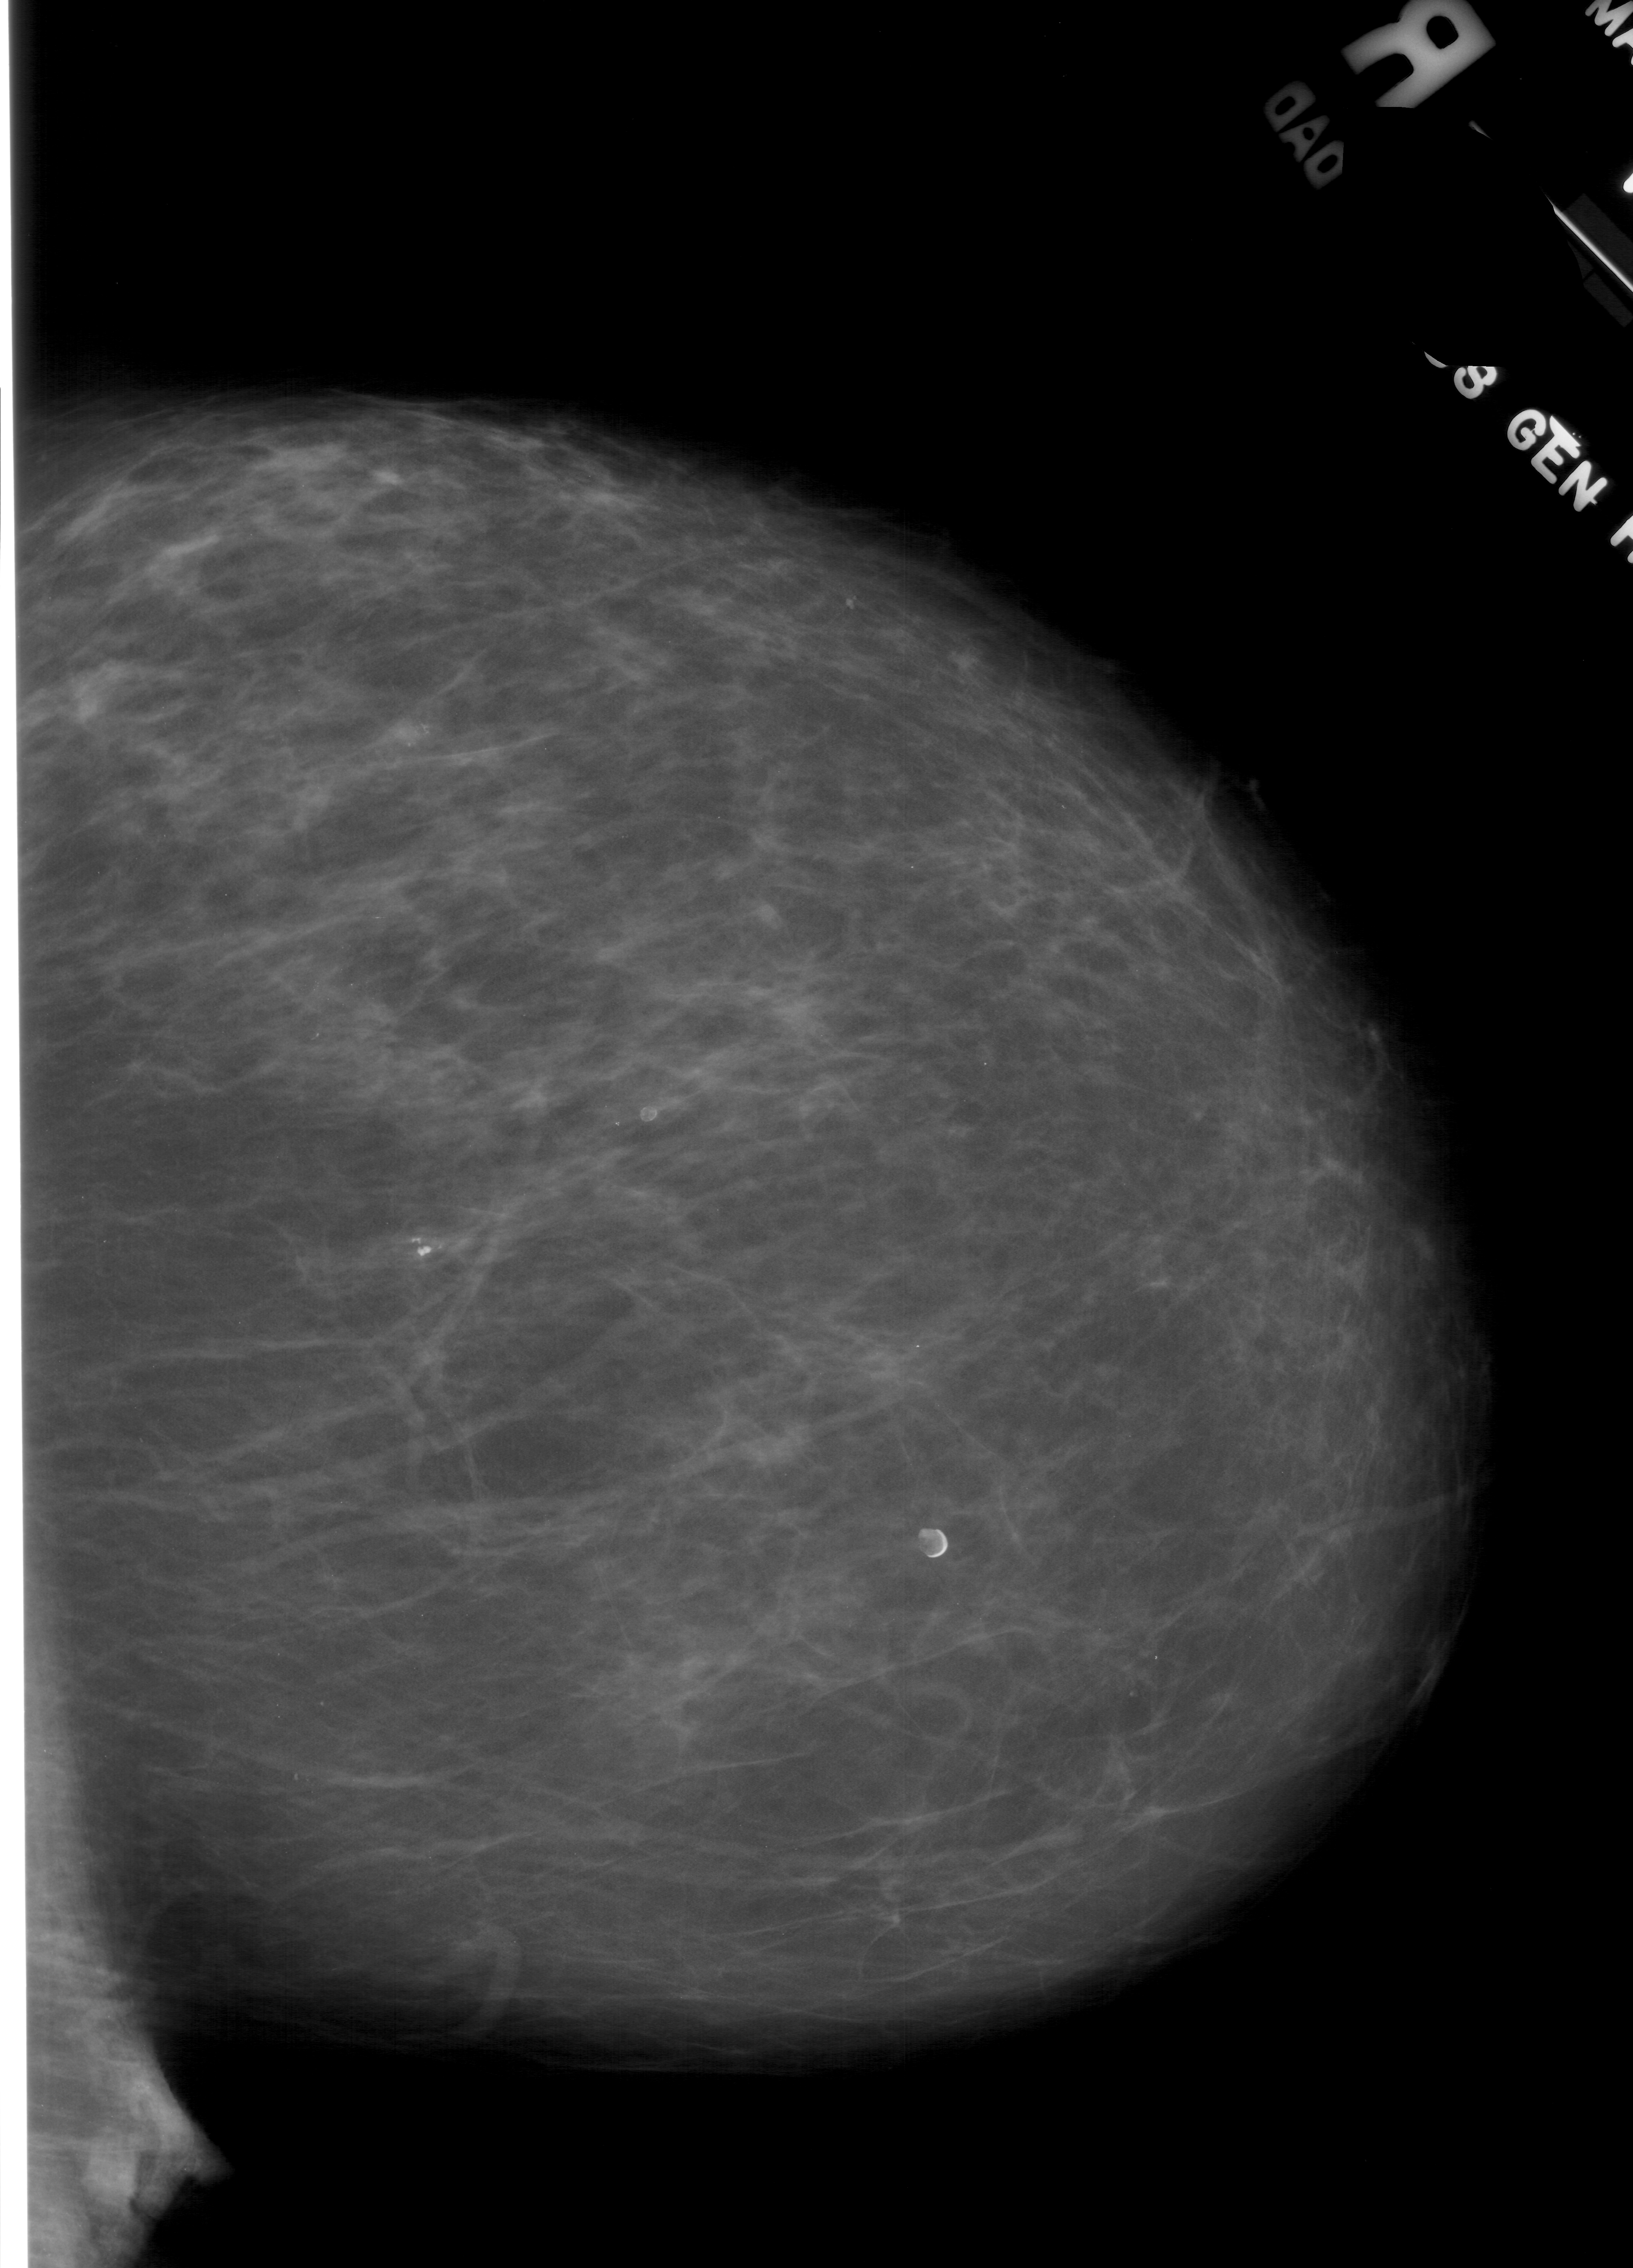
Scanned film-screen mammogram, right breast, CC view, BI-RADS breast density category 3 (scale 1–4).
Abnormality record for this image: calcifications, morphology pleomorphic, distribution clustered; BI-RADS assessment category 4; subtlety rating 2 on a 1 (subtle) to 5 (obvious) scale; pathology (as recorded): benign.